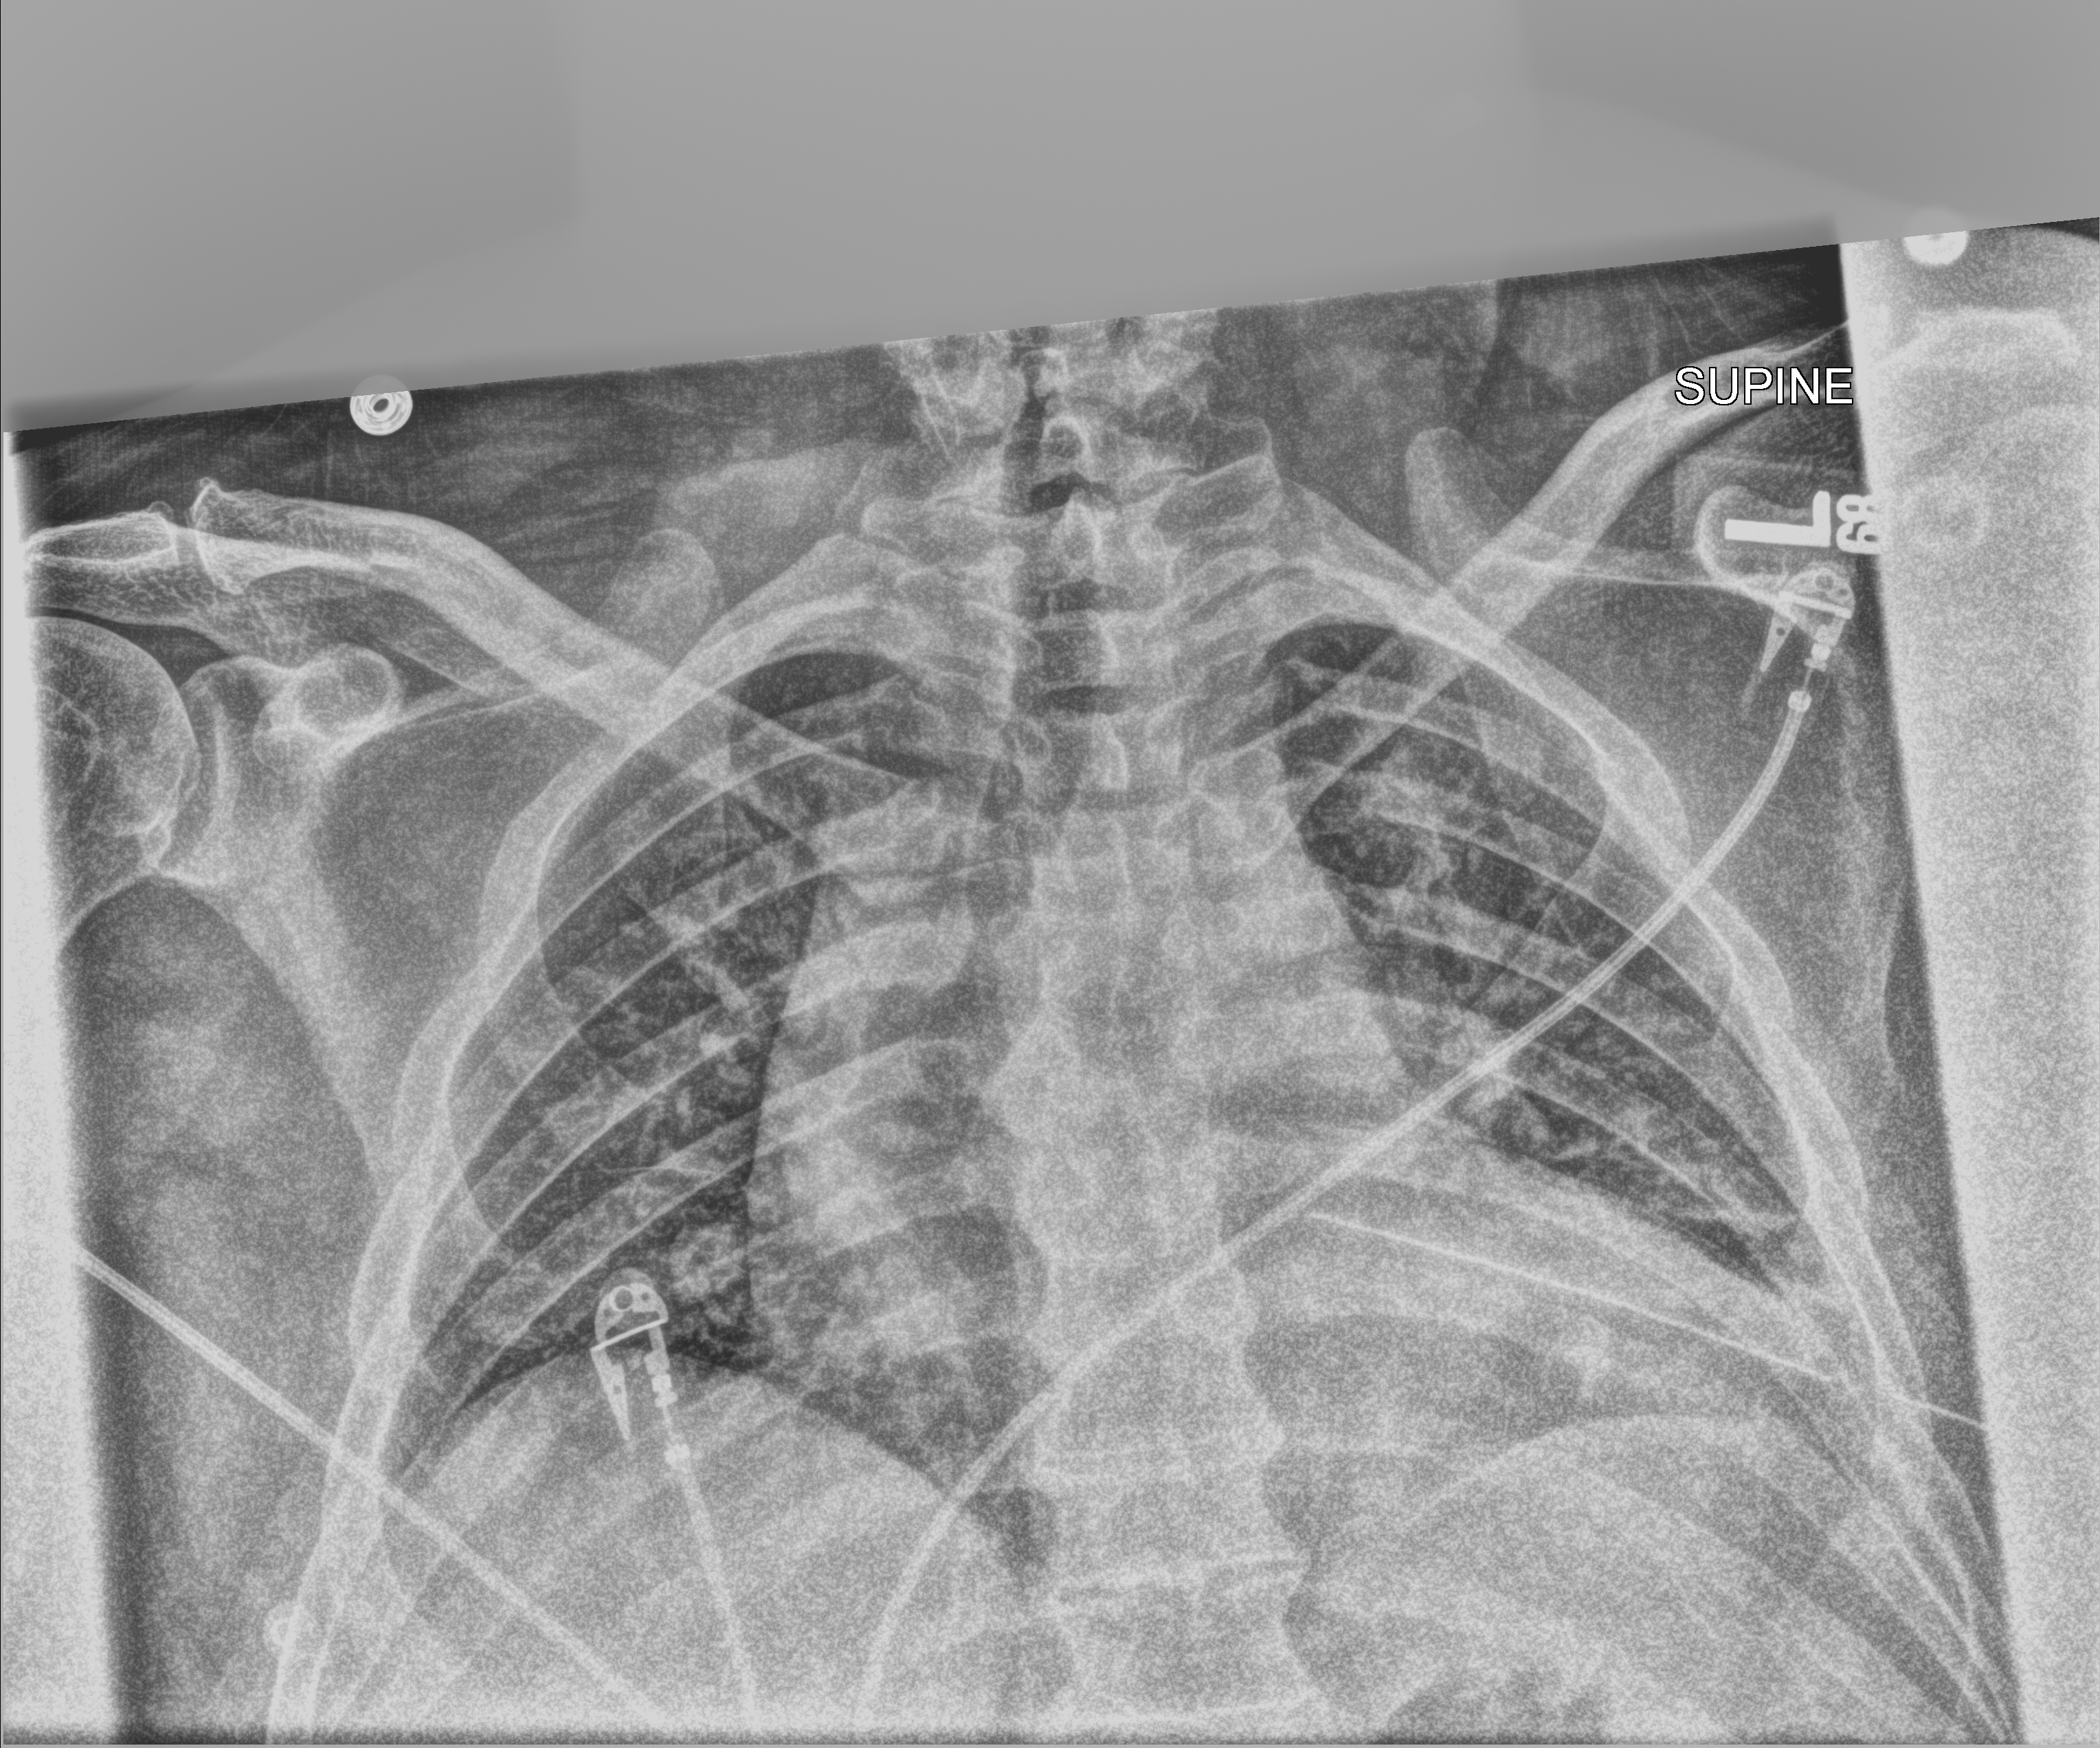
Chest X-ray (portable). Male patient hospitalised with COVID-19, age 18–59 years.
Admission-level facts for this patient (not findings on this image; timing relative to this image not recorded):
- mechanically ventilated during this hospital stay: no
- admitted to intensive care during this hospital stay: no